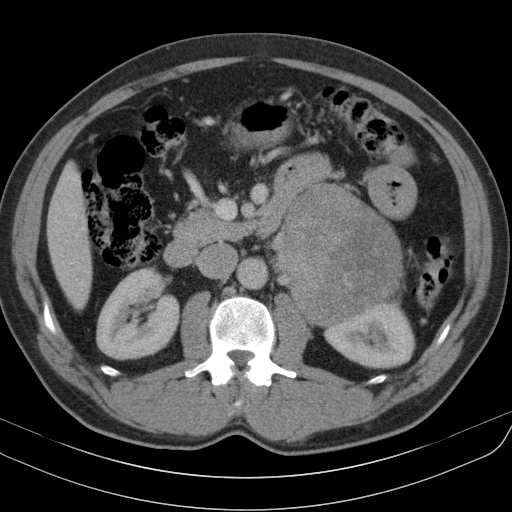
Contrast-enhanced abdominal CT, one axial slice; slice 59 of 91 in the series (ordered by position); 130 kVp; intravenous contrast given; soft-tissue window (W 400 / L 40 HU); 5 mm slice thickness; 512 × 512 image matrix. Male patient, age 51 years. From the clinical record (not read from this slice): diagnosis: adrenocortical carcinoma; tumour side: left adrenal.
Outlined on this slice (semi-automatically segmented with operator editing):
- mass: bounding box <281,186,405,325> (left, top, right, bottom; pixels)